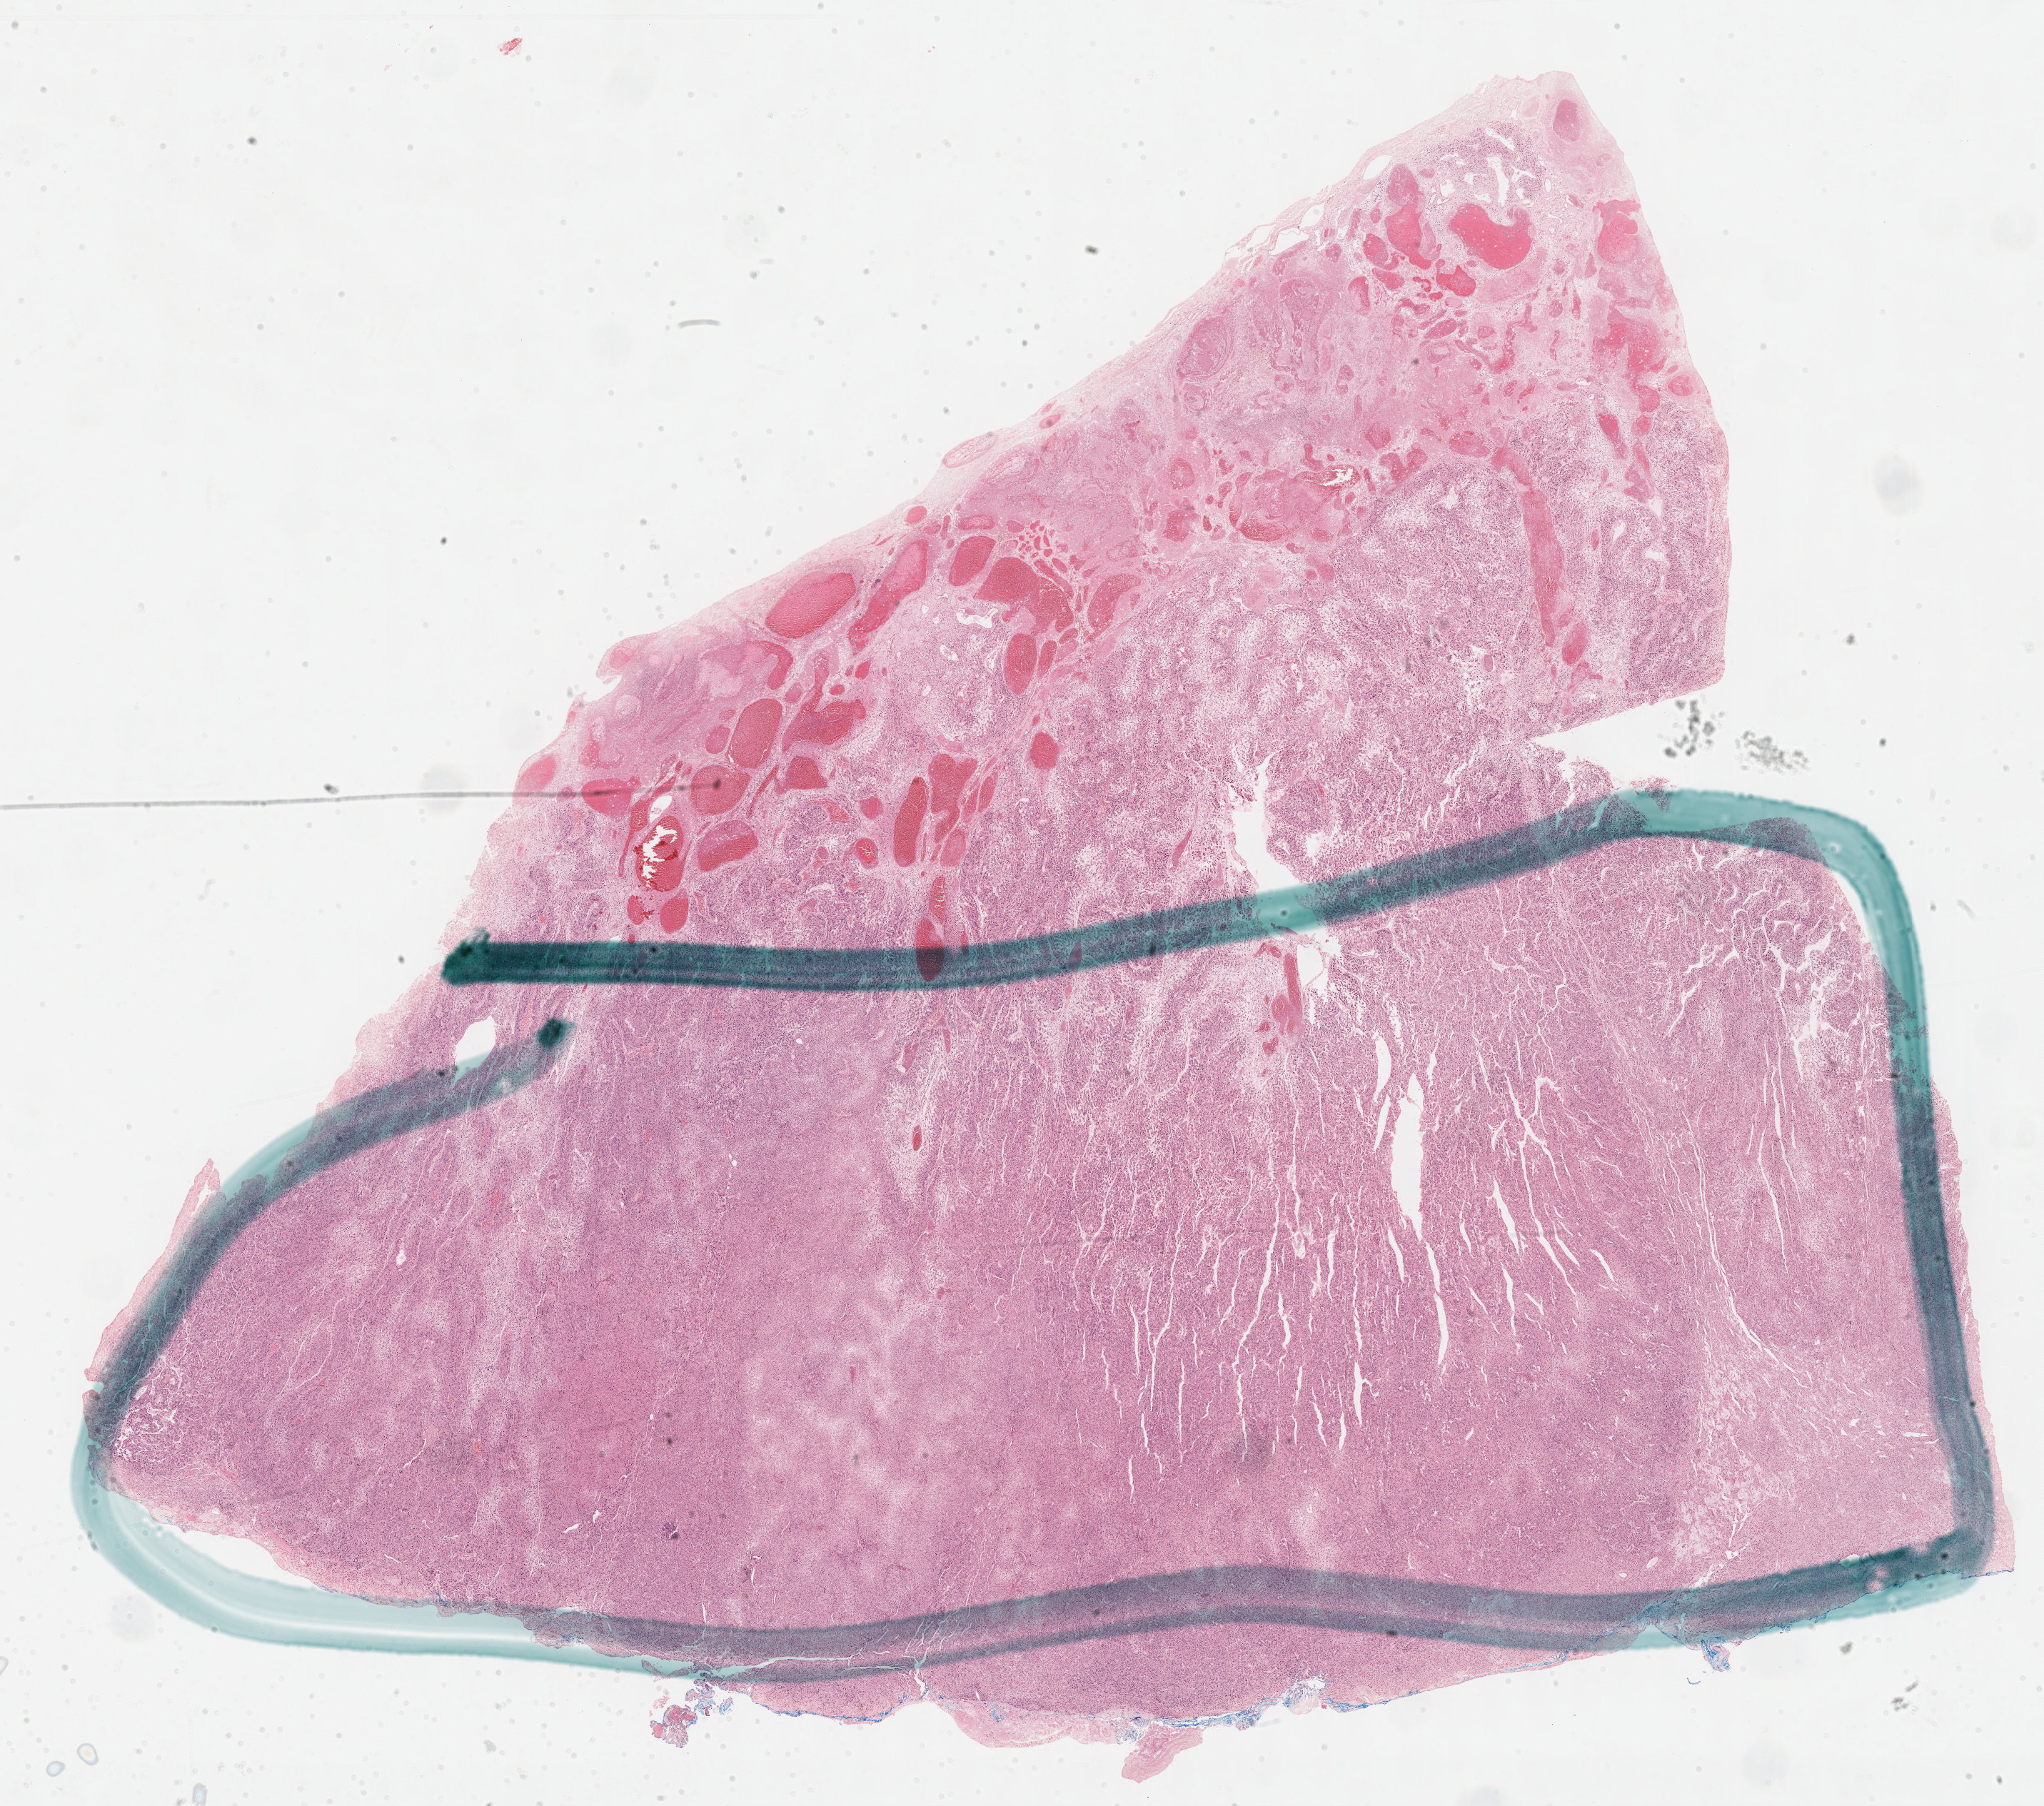
Digitized Hematoxylin and eosin (H&E) stained tissue section (whole slide) — low-resolution overview of the scanned area, about 23.1 x 20.4 mm; formalin-fixed paraffin-embedded (FFPE) diagnostic section; primary tumour sample from the adrenal cortex. Patient: female, age at initial diagnosis 61 years.
- diagnosis: Adrenal cortical carcinoma (cortex of adrenal gland)